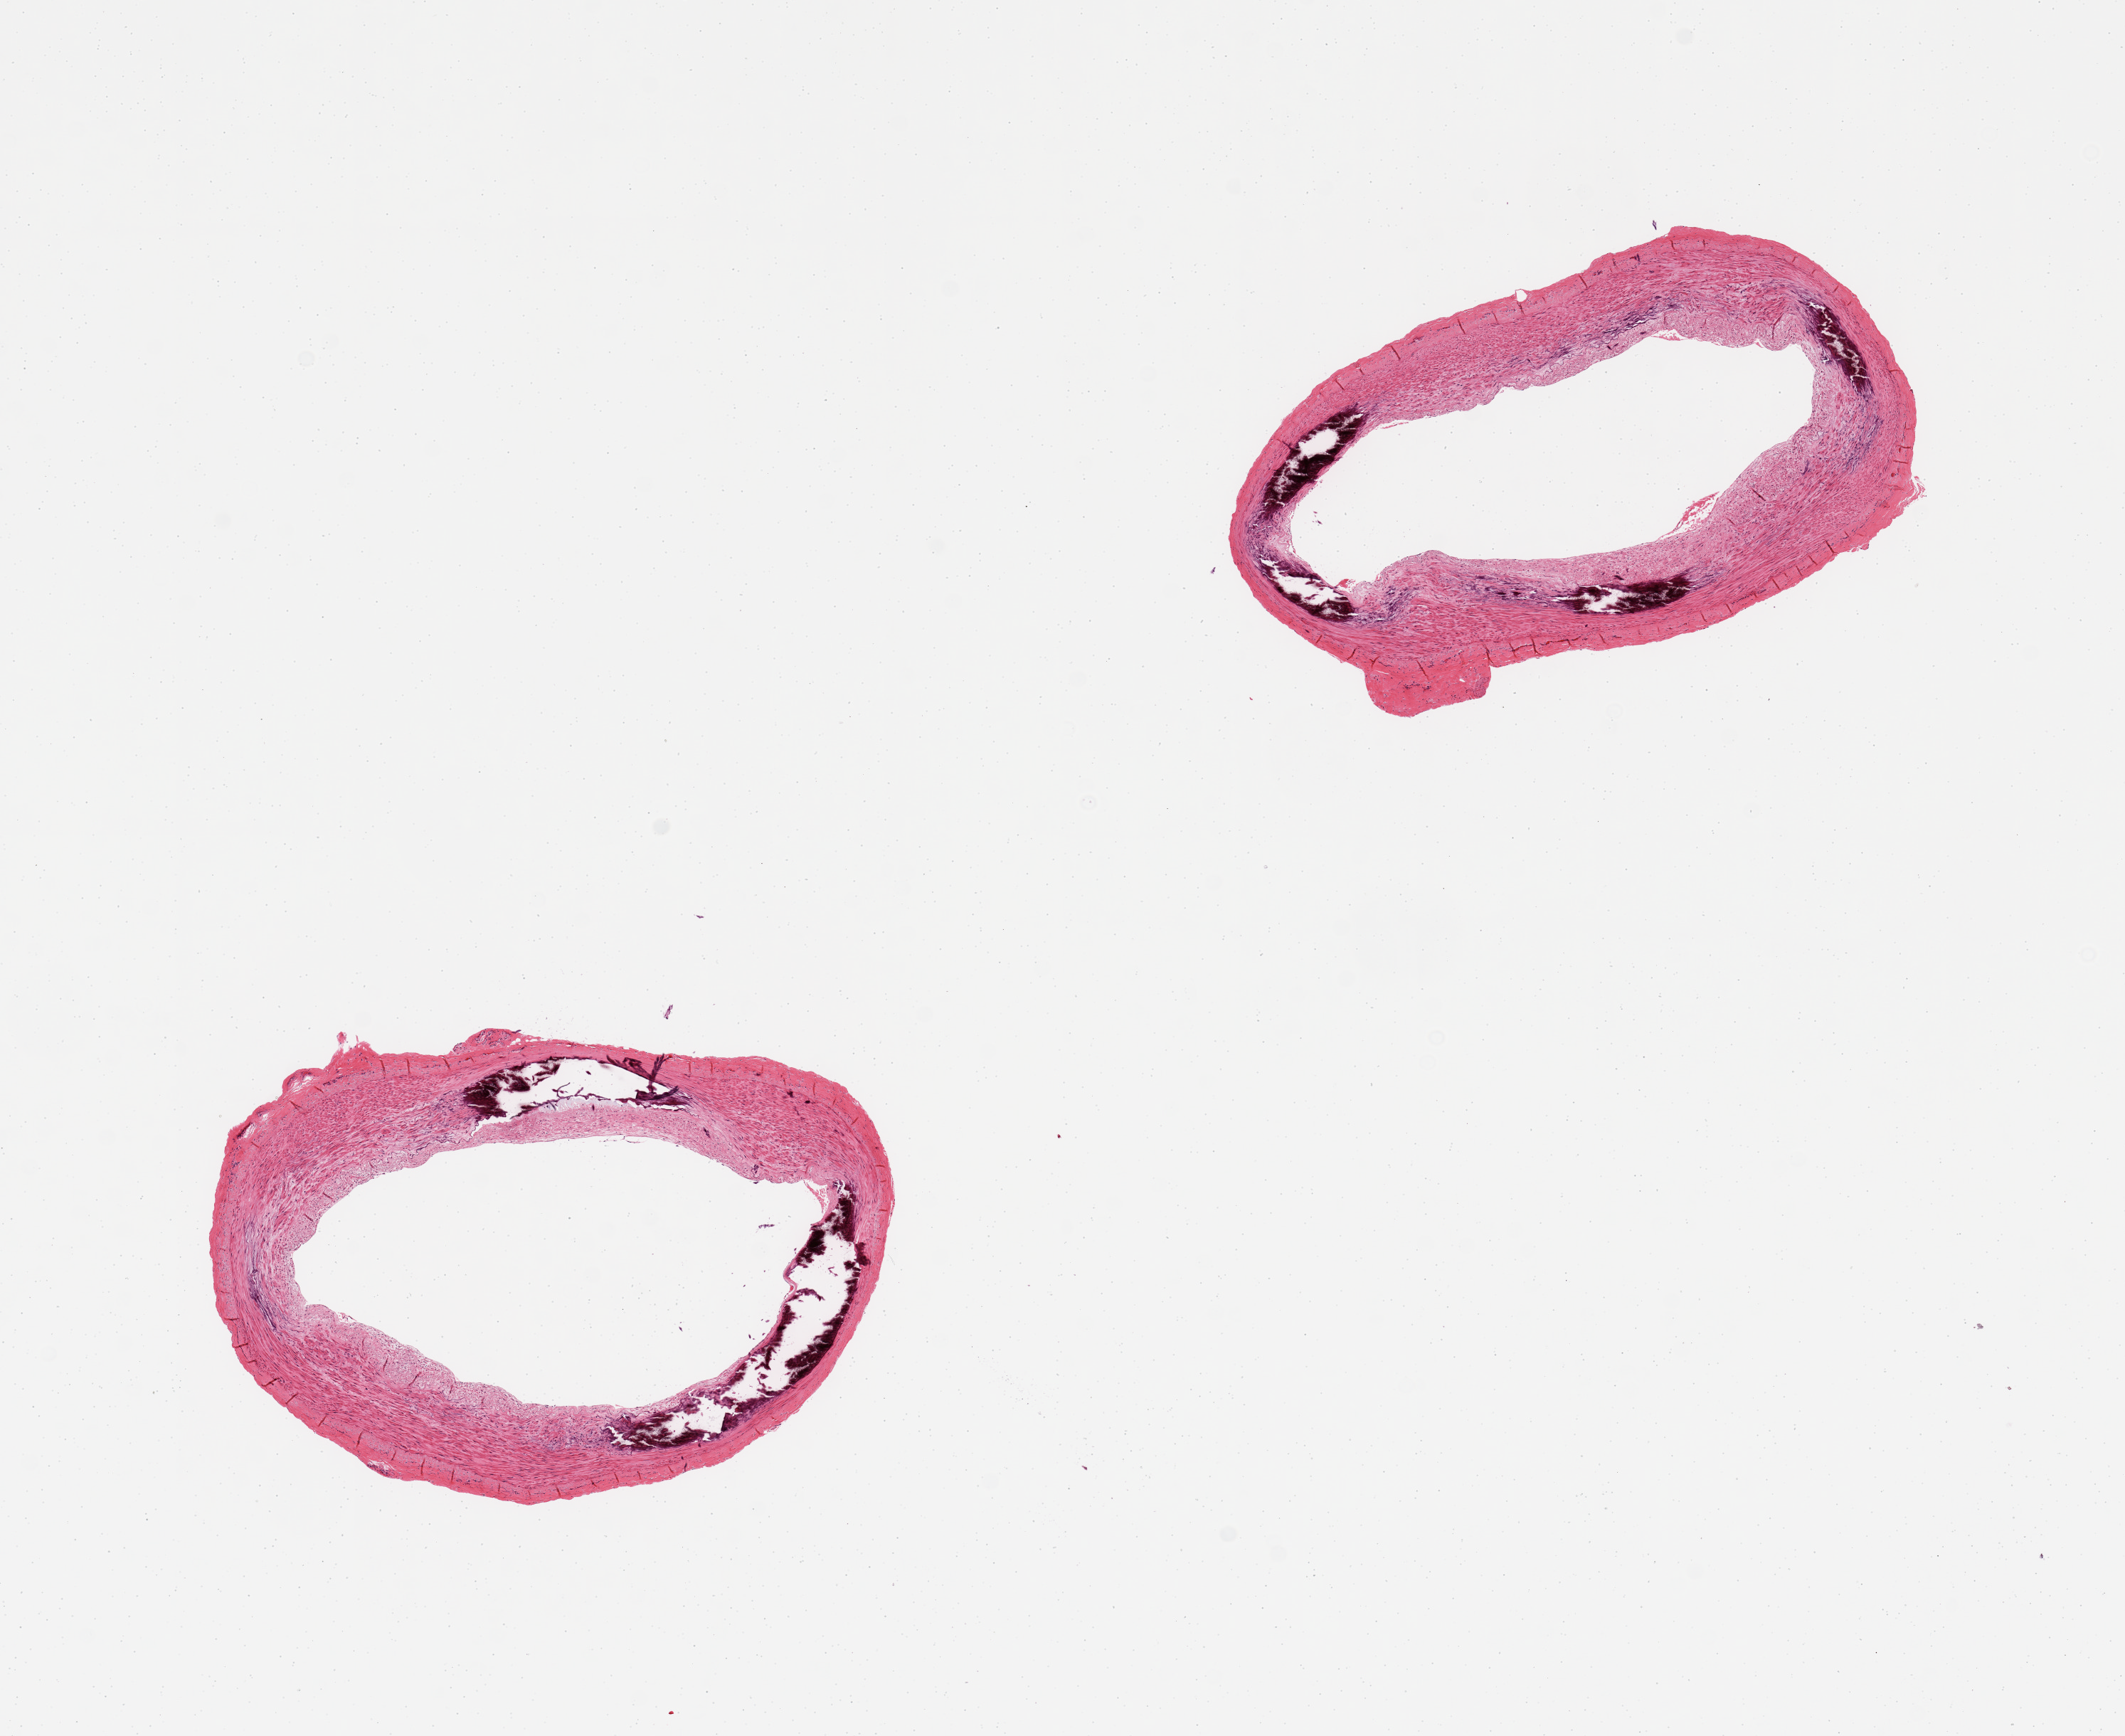
Whole-slide image, hematoxylin and eosin (H&E) stain — whole scanned area (about 11.8 x 9.6 mm, slide scanned at 20x) shown as a low-resolution overview. PAXgene-fixed paraffin-embedded (PFPE) section. Target tissue: tibial artery. Donor tissue sample. Male donor.
Pathologist's review note for this sample: 2 pieces, medial calcific sclerosis (Monckeberg's sclerosis), both sections.